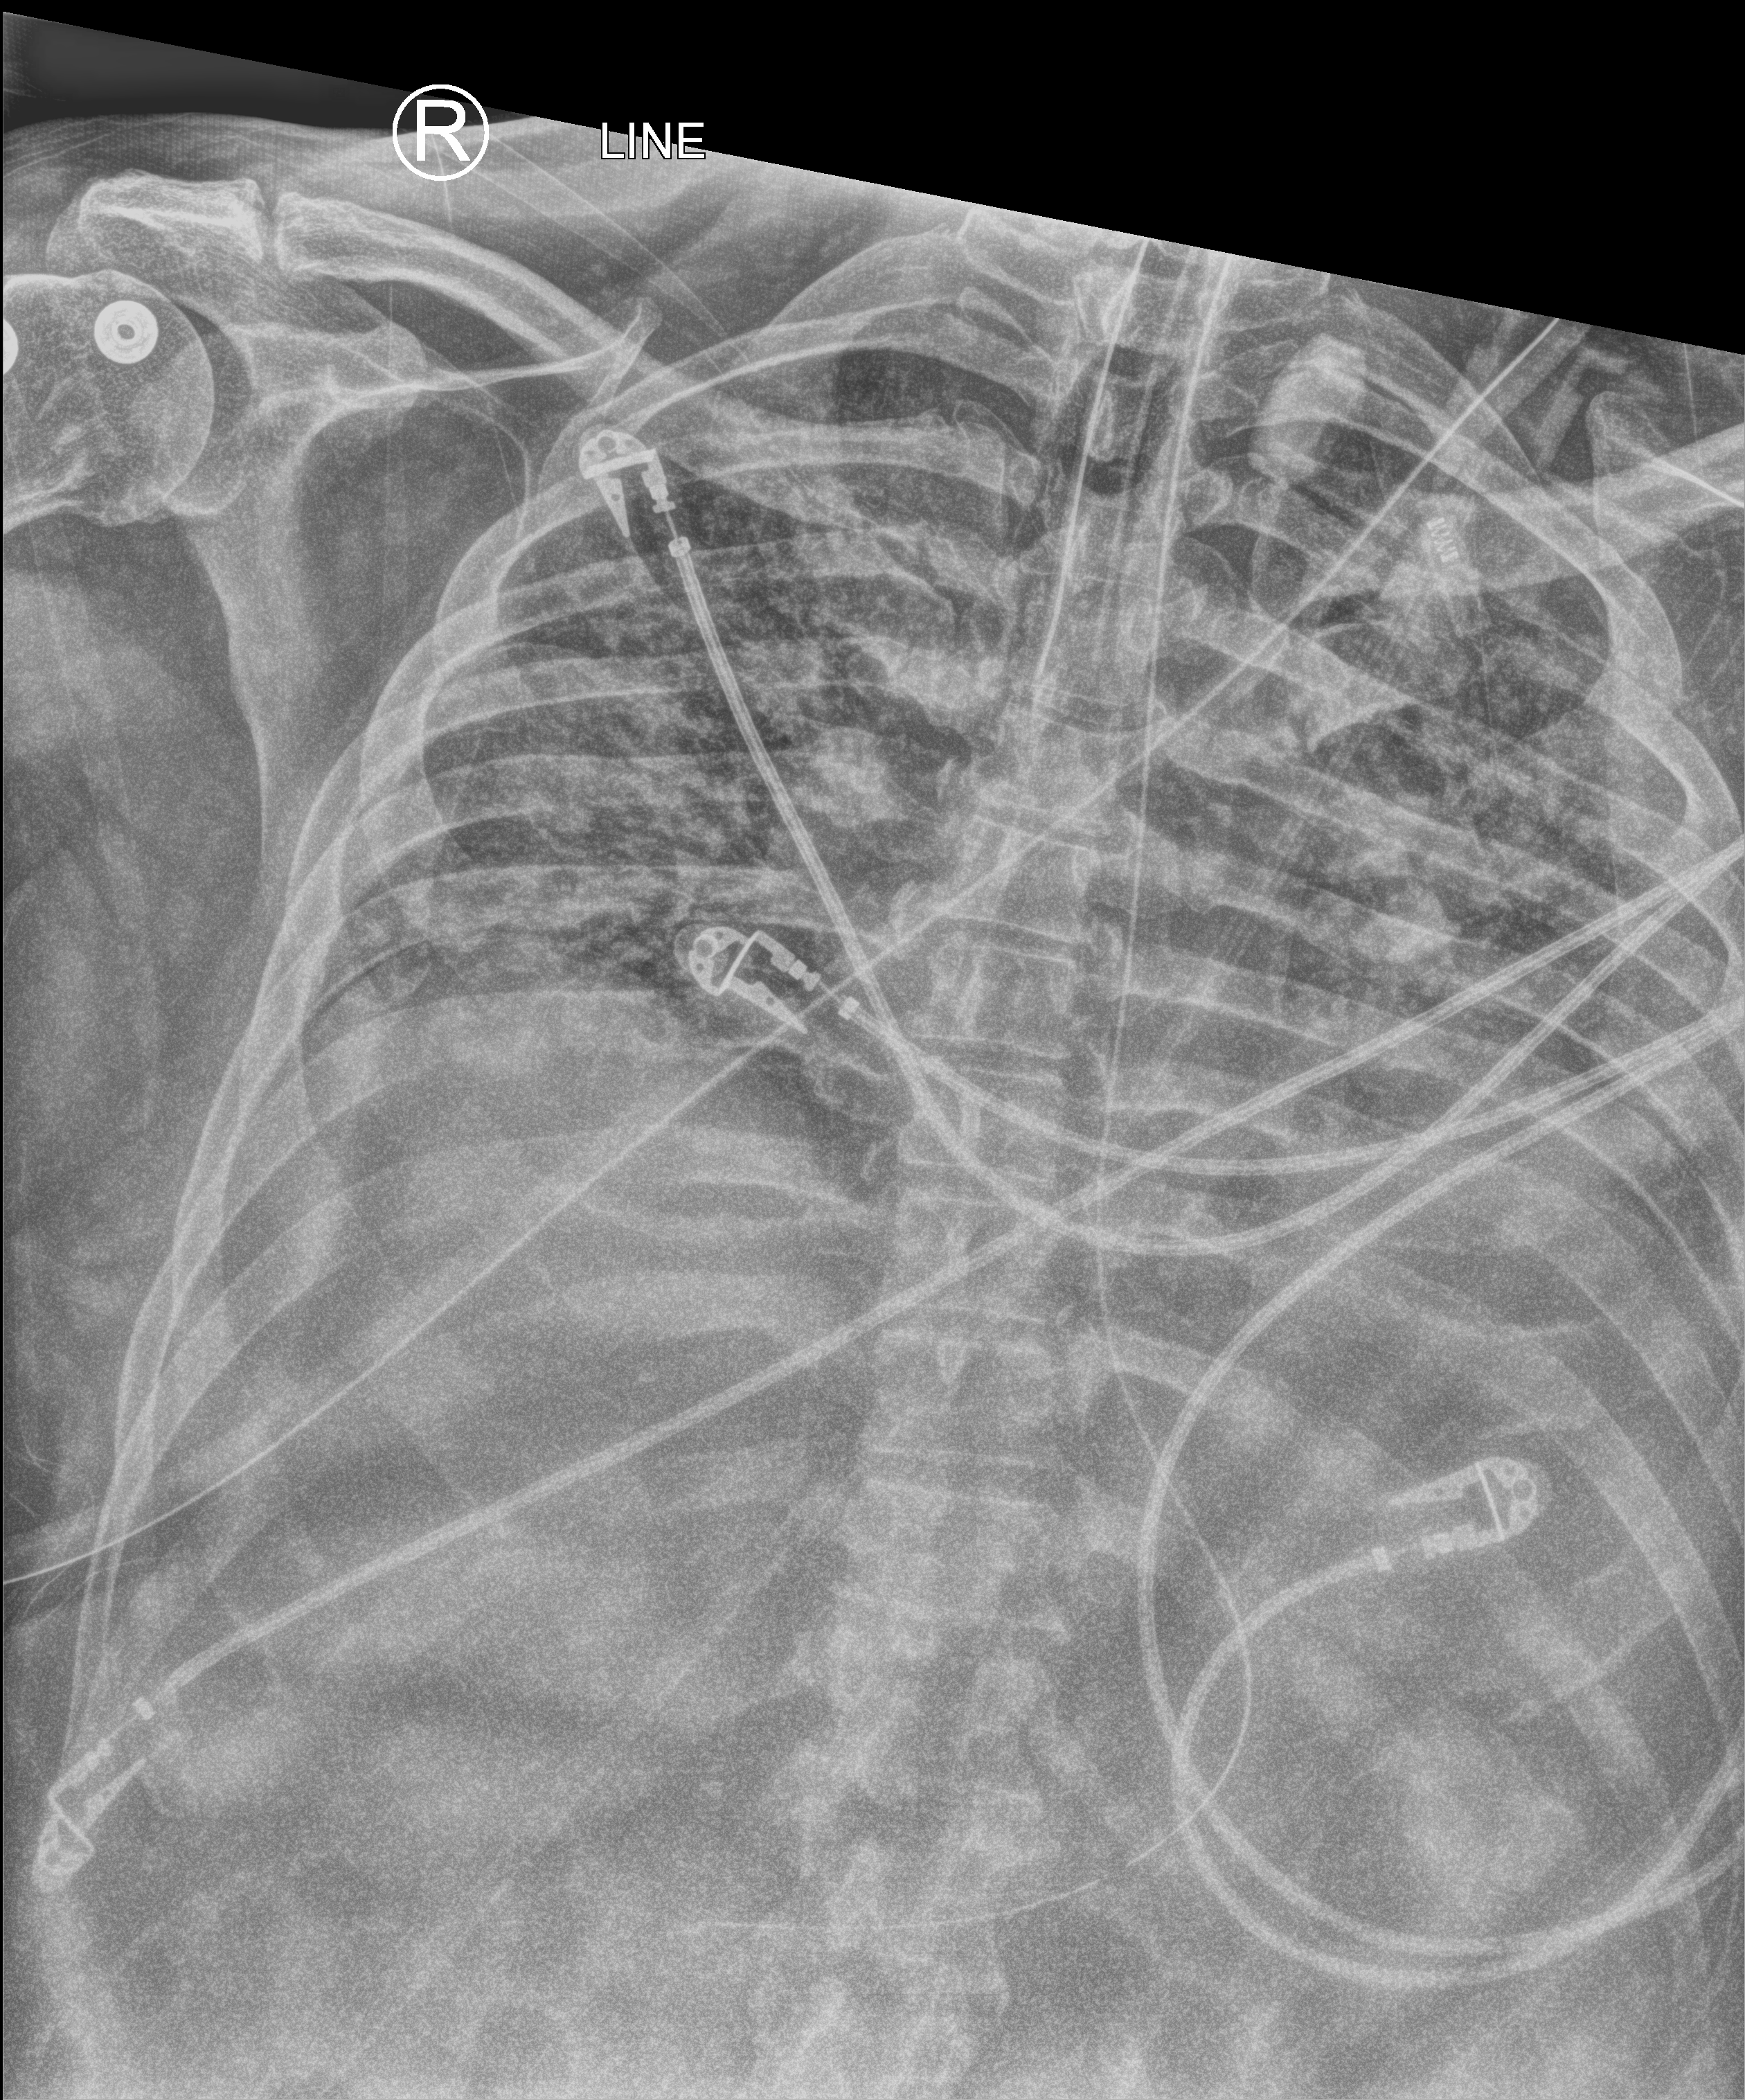
Portable chest radiograph; anteroposterior (AP) projection. Patient hospitalised with COVID-19; male, aged 18–59 years.
From the hospital-stay record, not from the radiograph (when in the stay this image was taken is not recorded): admitted to intensive care during this hospital stay: yes.